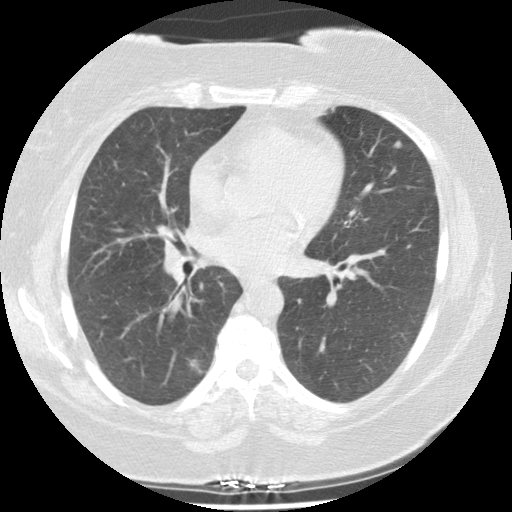
Axial slice from a low-dose chest CT screening exam; second screening round (one year after baseline); lung window (W 1500 / L -600 HU); standard (soft-tissue) reconstruction kernel (STANDARD); slice 55 of 131 in the series. Female participant, aged 58 years at enrolment. Current smoker at enrolment.
Expert reader's lesion annotation, bounding box [x1, y1, x2, y2] px = [165, 338, 218, 400]. The screening reader recorded 4 non-calcified nodules or masses ≥4 mm on this exam; which of them this box marks is not recorded. Official screen result: positive, other. Participant outcome: lung cancer diagnosed 299 days after this screen — adenocarcinoma, NOS, right lower lobe, stage IIIA (AJCC 6th edition), 25 mm at pathology.